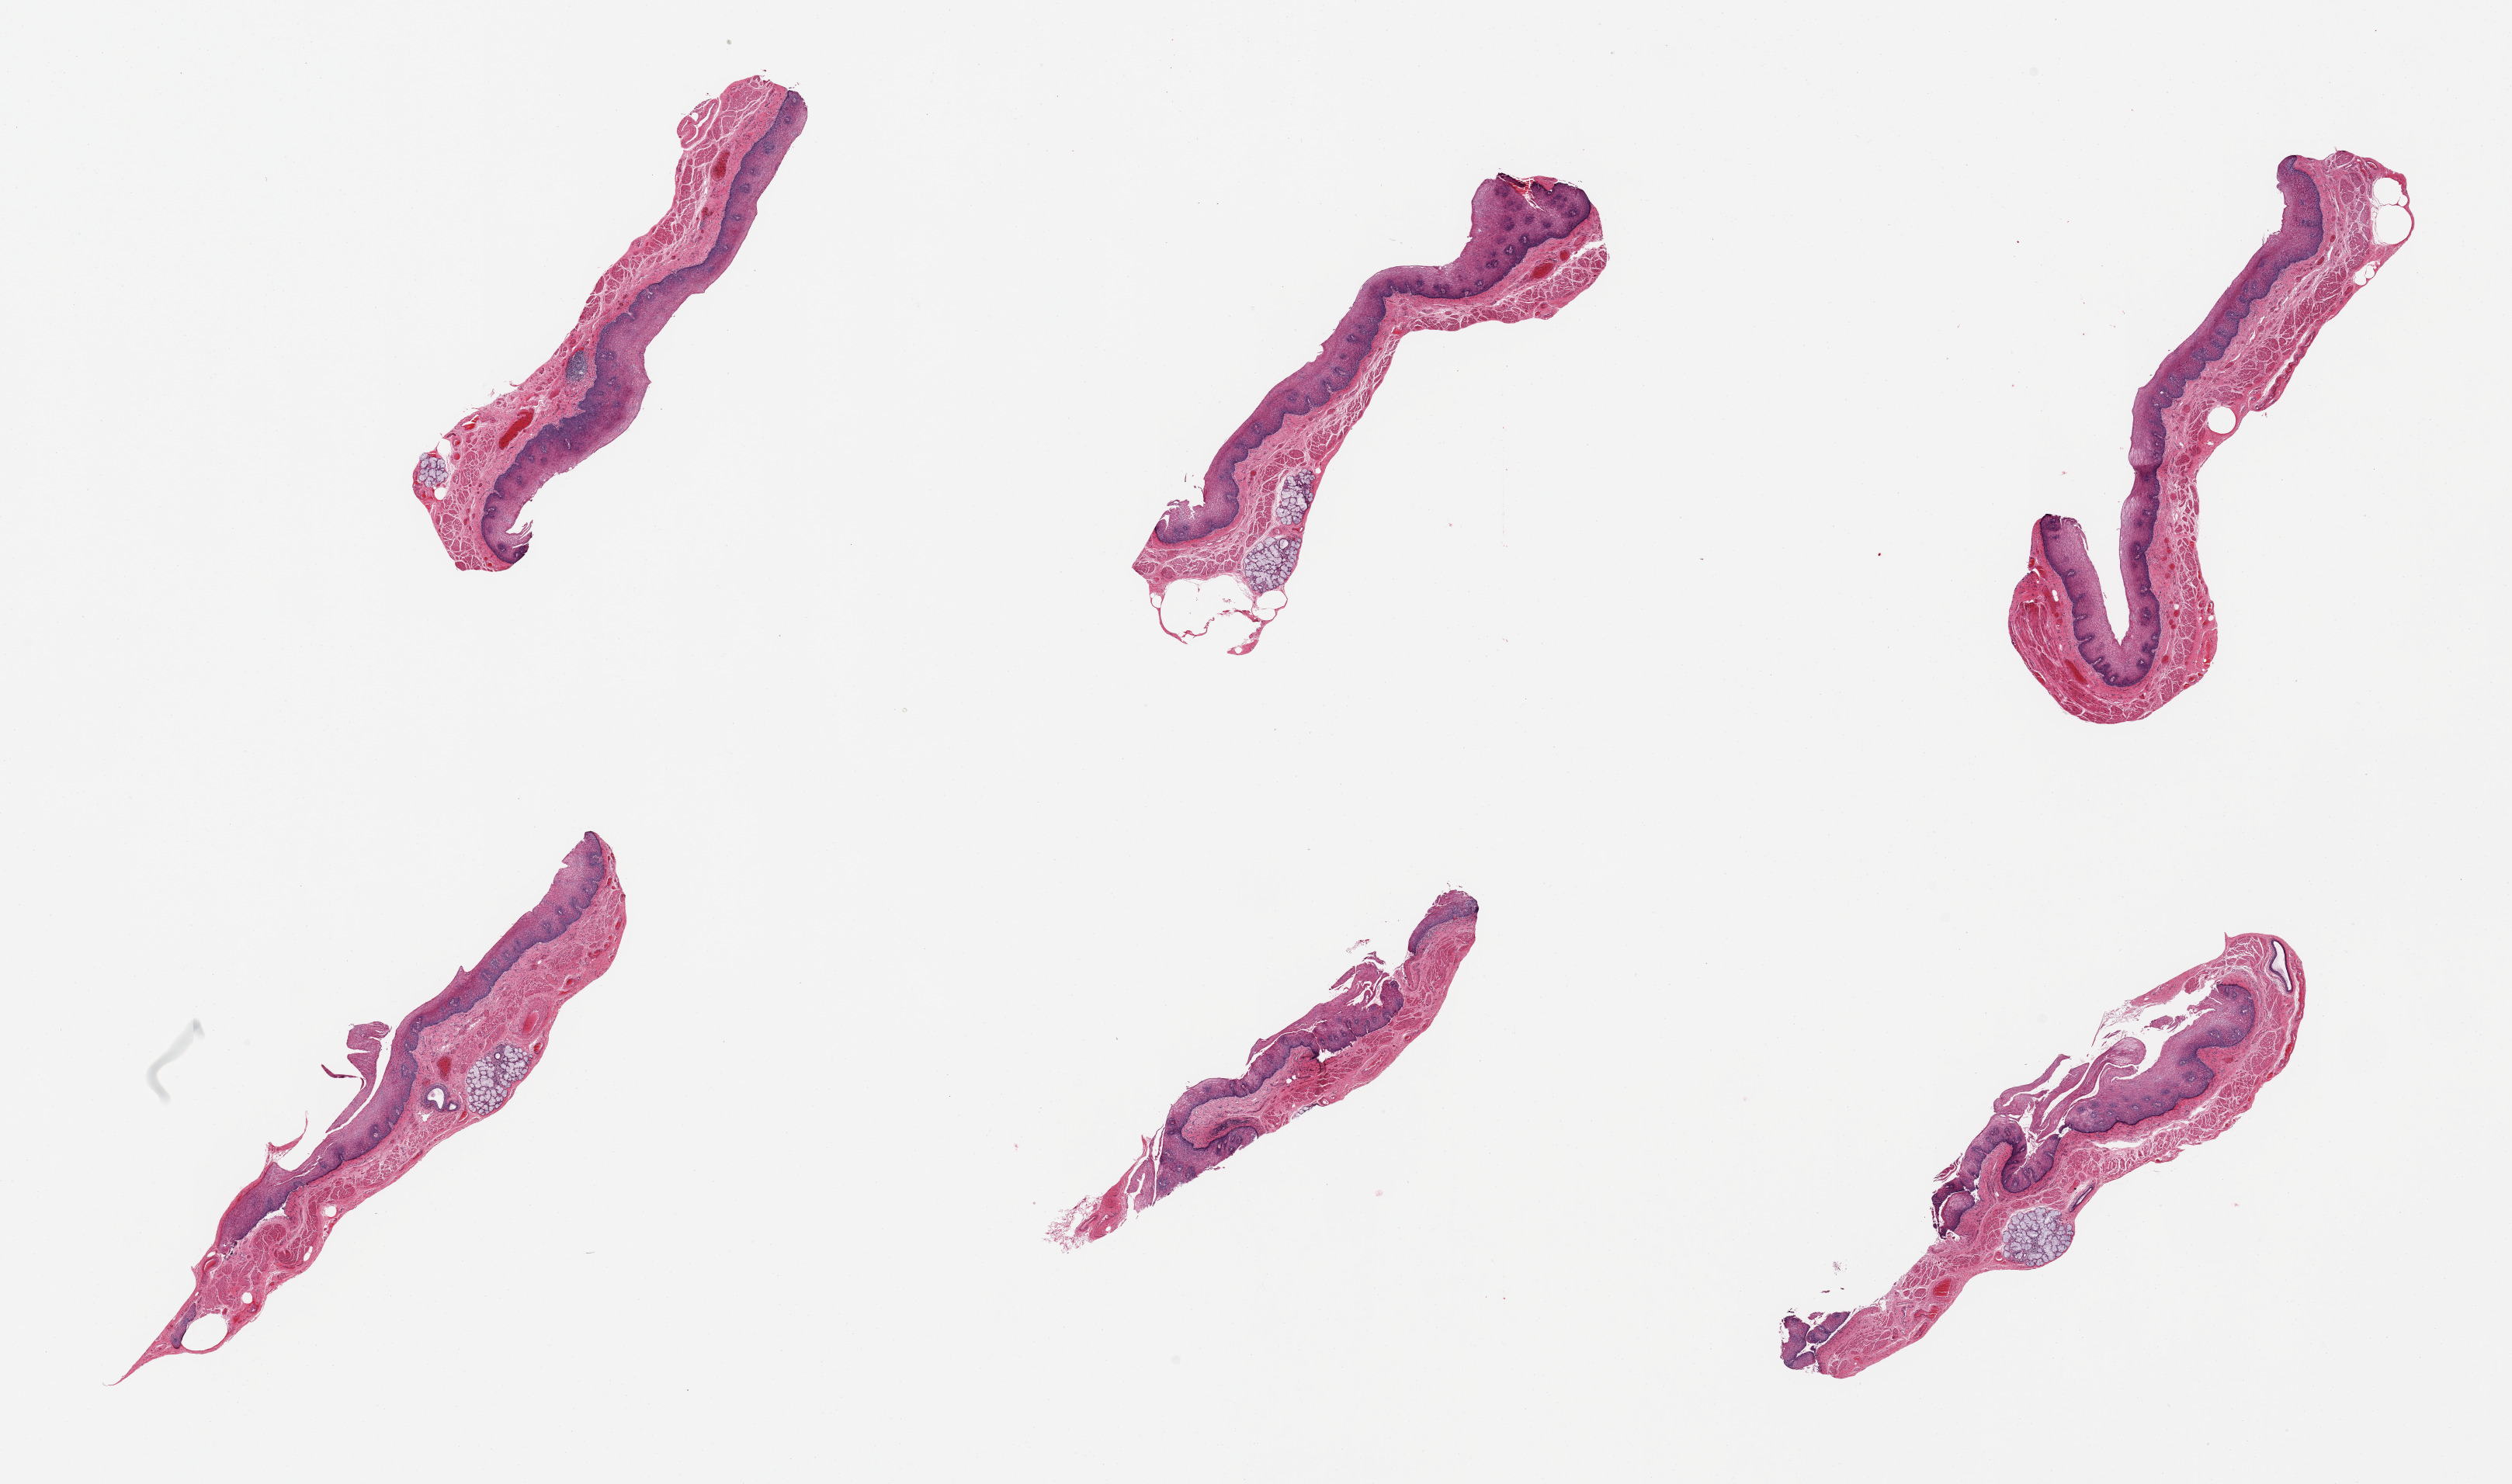
H&E whole-slide image, low-resolution overview of the scanned area, about 25.6 x 15.1 mm. PAXgene-fixed paraffin-embedded (PFPE) section. Sampled site (target tissue): esophageal mucous membrane. Tissue donor sample. Female donor.
Review note (as recorded): 6 pieces; well dissected.